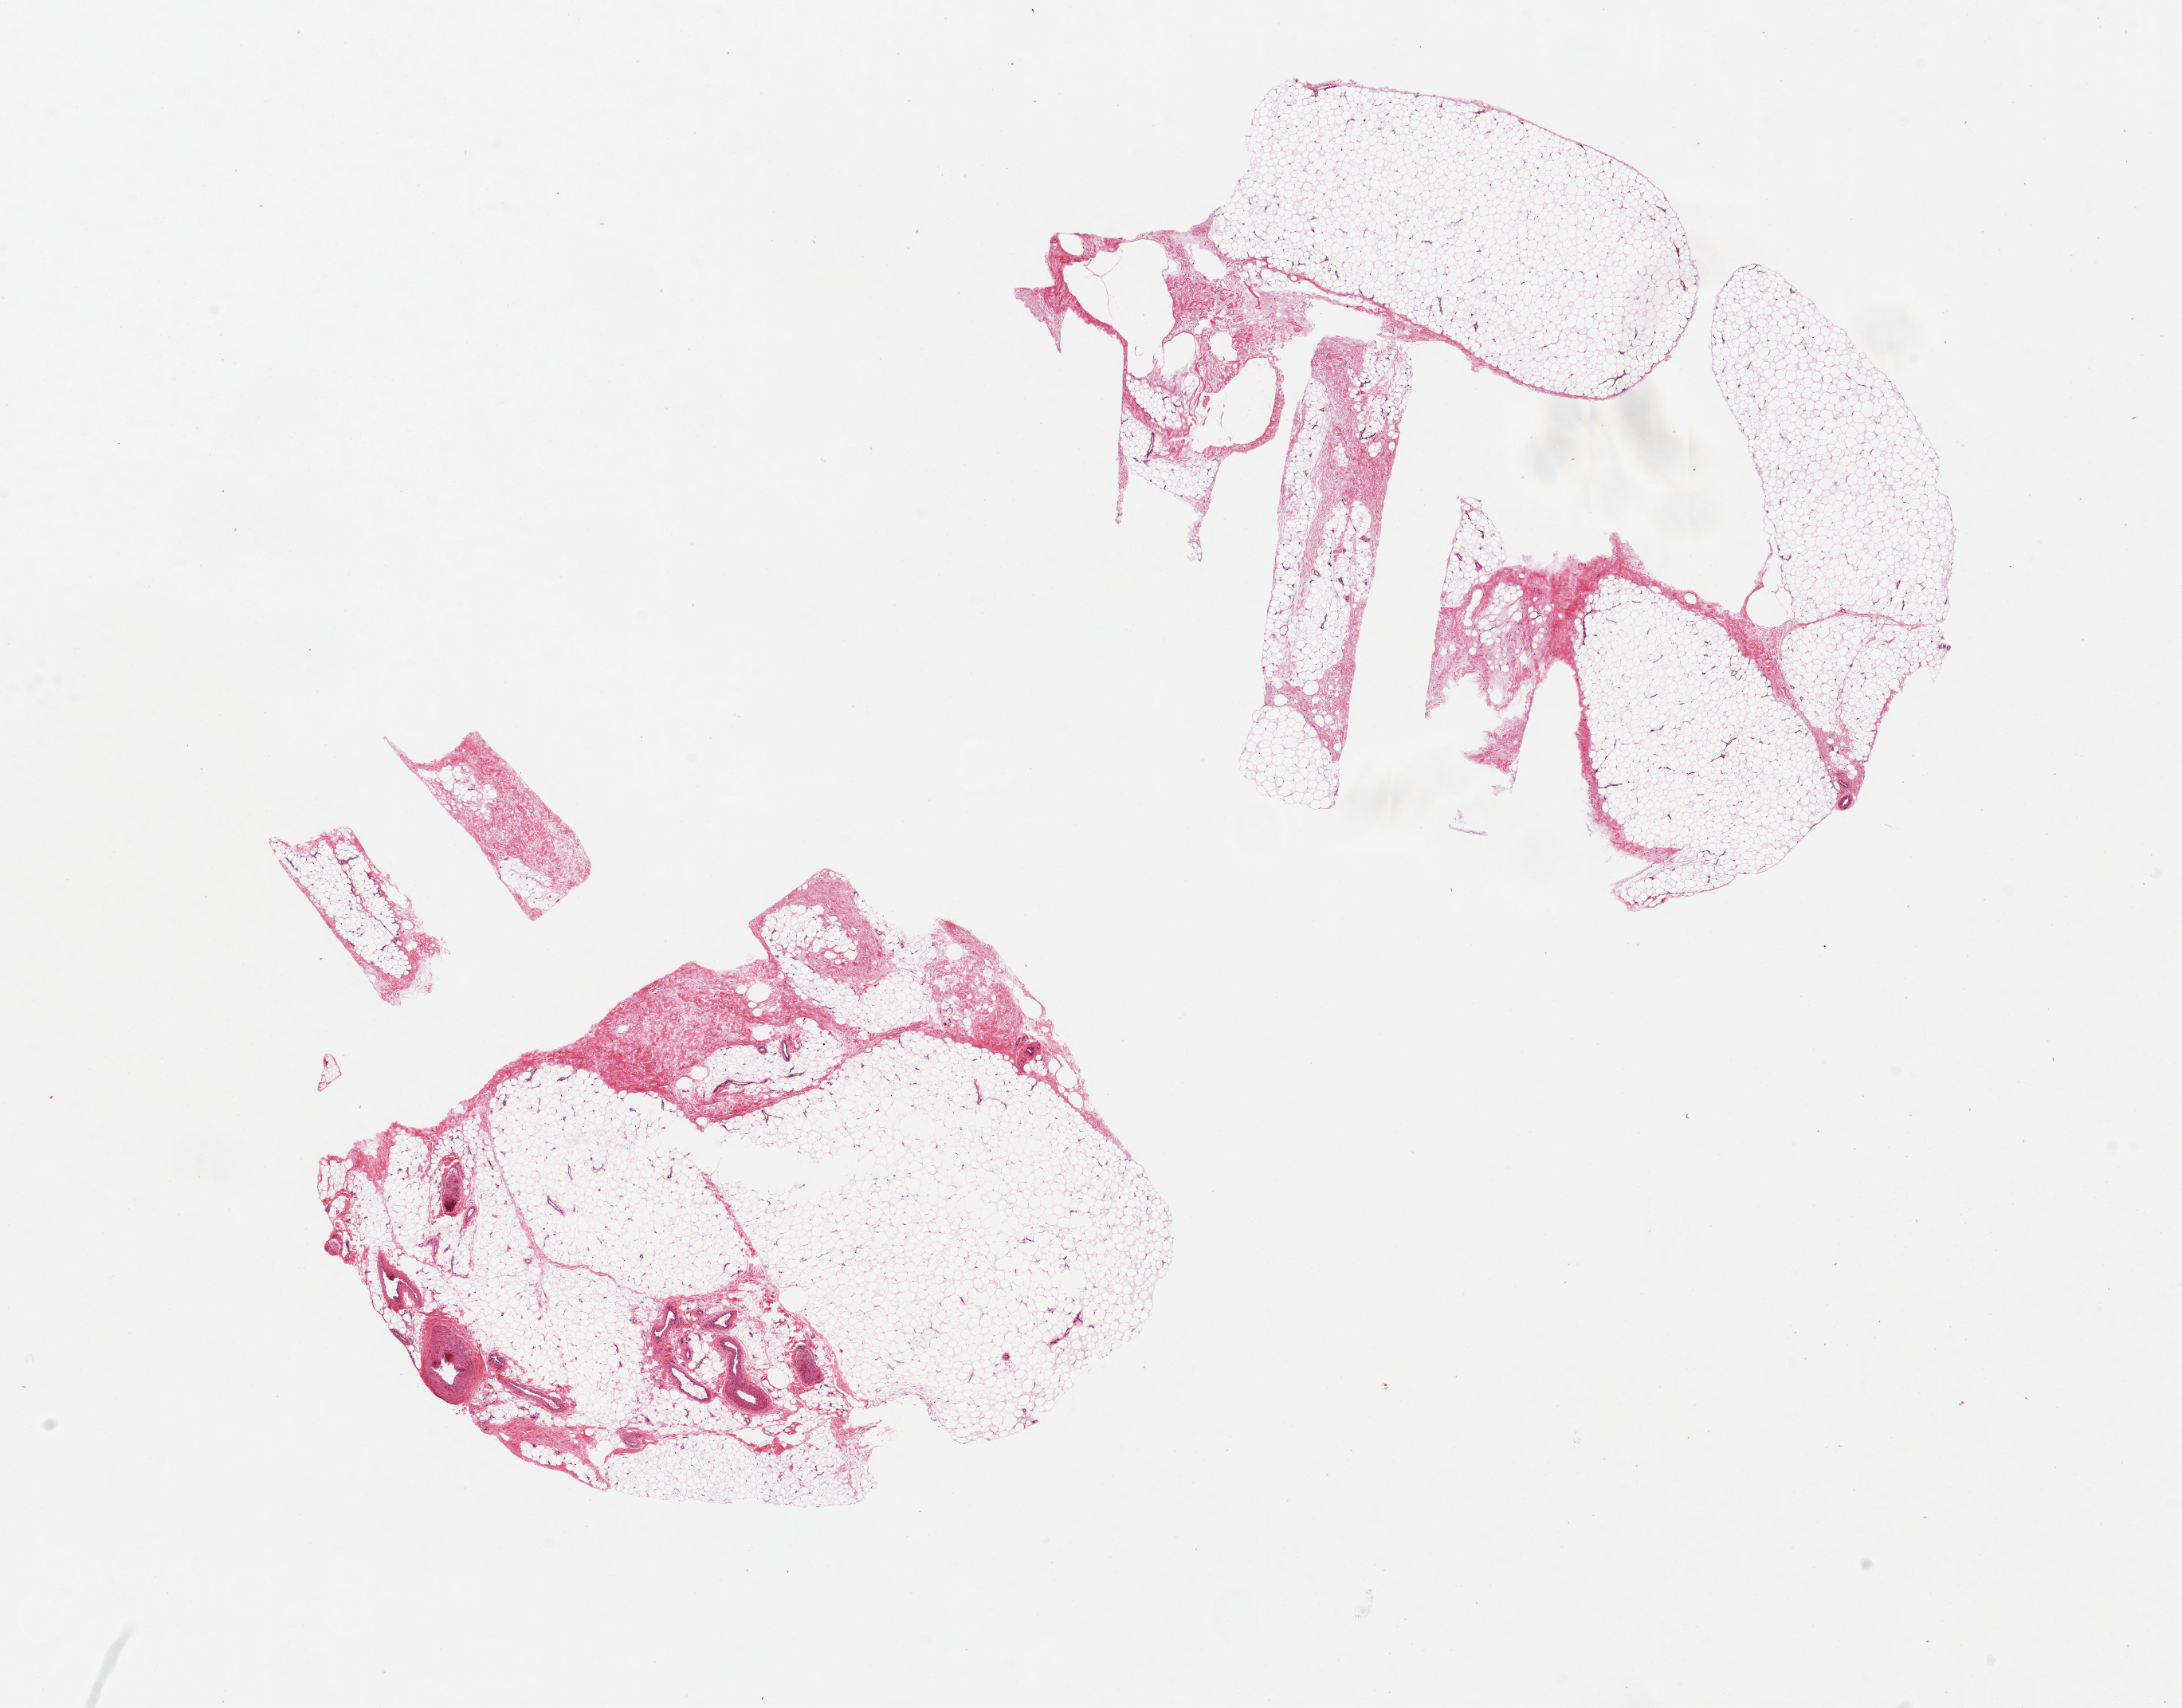
Whole-slide image, H&E stain — whole scanned area (about 21.7 x 17.0 mm, slide scanned at 20x) shown as a low-resolution overview. PAXgene-fixed paraffin-embedded (PFPE) section. Sampled site (target tissue): adipose tissue. Donor tissue sample. Donor sex: male.
Pathologist's review note for this sample: 2 pieces, 6.5x5.5 & 8x6mm; cassette indentations.